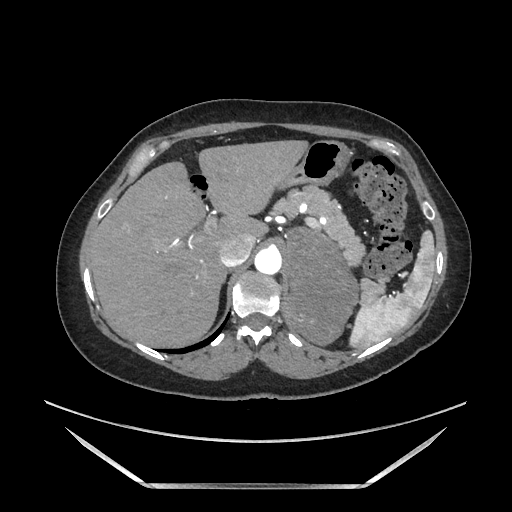
Contrast-enhanced abdominal CT, one axial slice. Position 130 of 205 along the scan axis. Soft-tissue window (W 400 / L 40 HU). 512 × 512 image matrix, field of view 440 × 440 mm. Female patient. Case-level facts recorded for this patient, not image findings: diagnosis: adrenocortical carcinoma; tumour side: left adrenal; tumour size at pathology: 12.5 cm; Ki-67 index: 39 %; stage (as recorded): 3.
Annotated regions visible in this slice (semi-automatically segmented with operator editing):
- mass: bounding box [x1, y1, x2, y2] px = [285, 228, 357, 343]